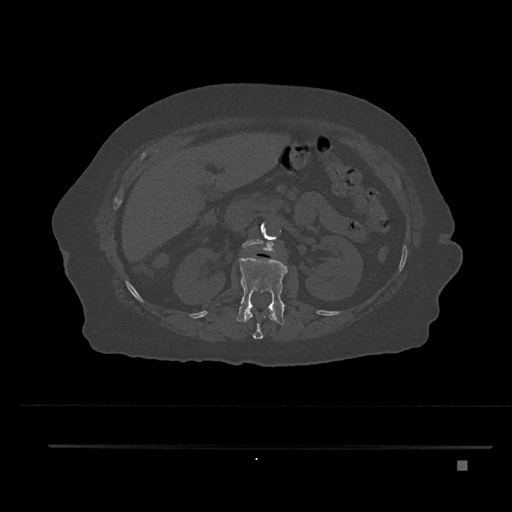
CT including the spine, one axial slice. Slice 226 of 797 in the series (ordered by position). Reconstruction kernel Br40s/3. Bone window (W 1800 / L 400 HU). 0.5 mm slice thickness. 512 × 512 image matrix, field of view 437 × 437 mm. Patient: female, 76 years. Case-level facts recorded for this patient, not image findings: primary cancer: lung; vertebrae with lytic lesions (as recorded): T11, L3.
Annotated regions visible in this slice (semi-automatically segmented with operator editing):
- L1 vertebra: bounding box <236,255,288,325> (left, top, right, bottom; pixels)
- L2 vertebra: <242,239,275,253>
- T12 vertebra: <244,308,277,339>